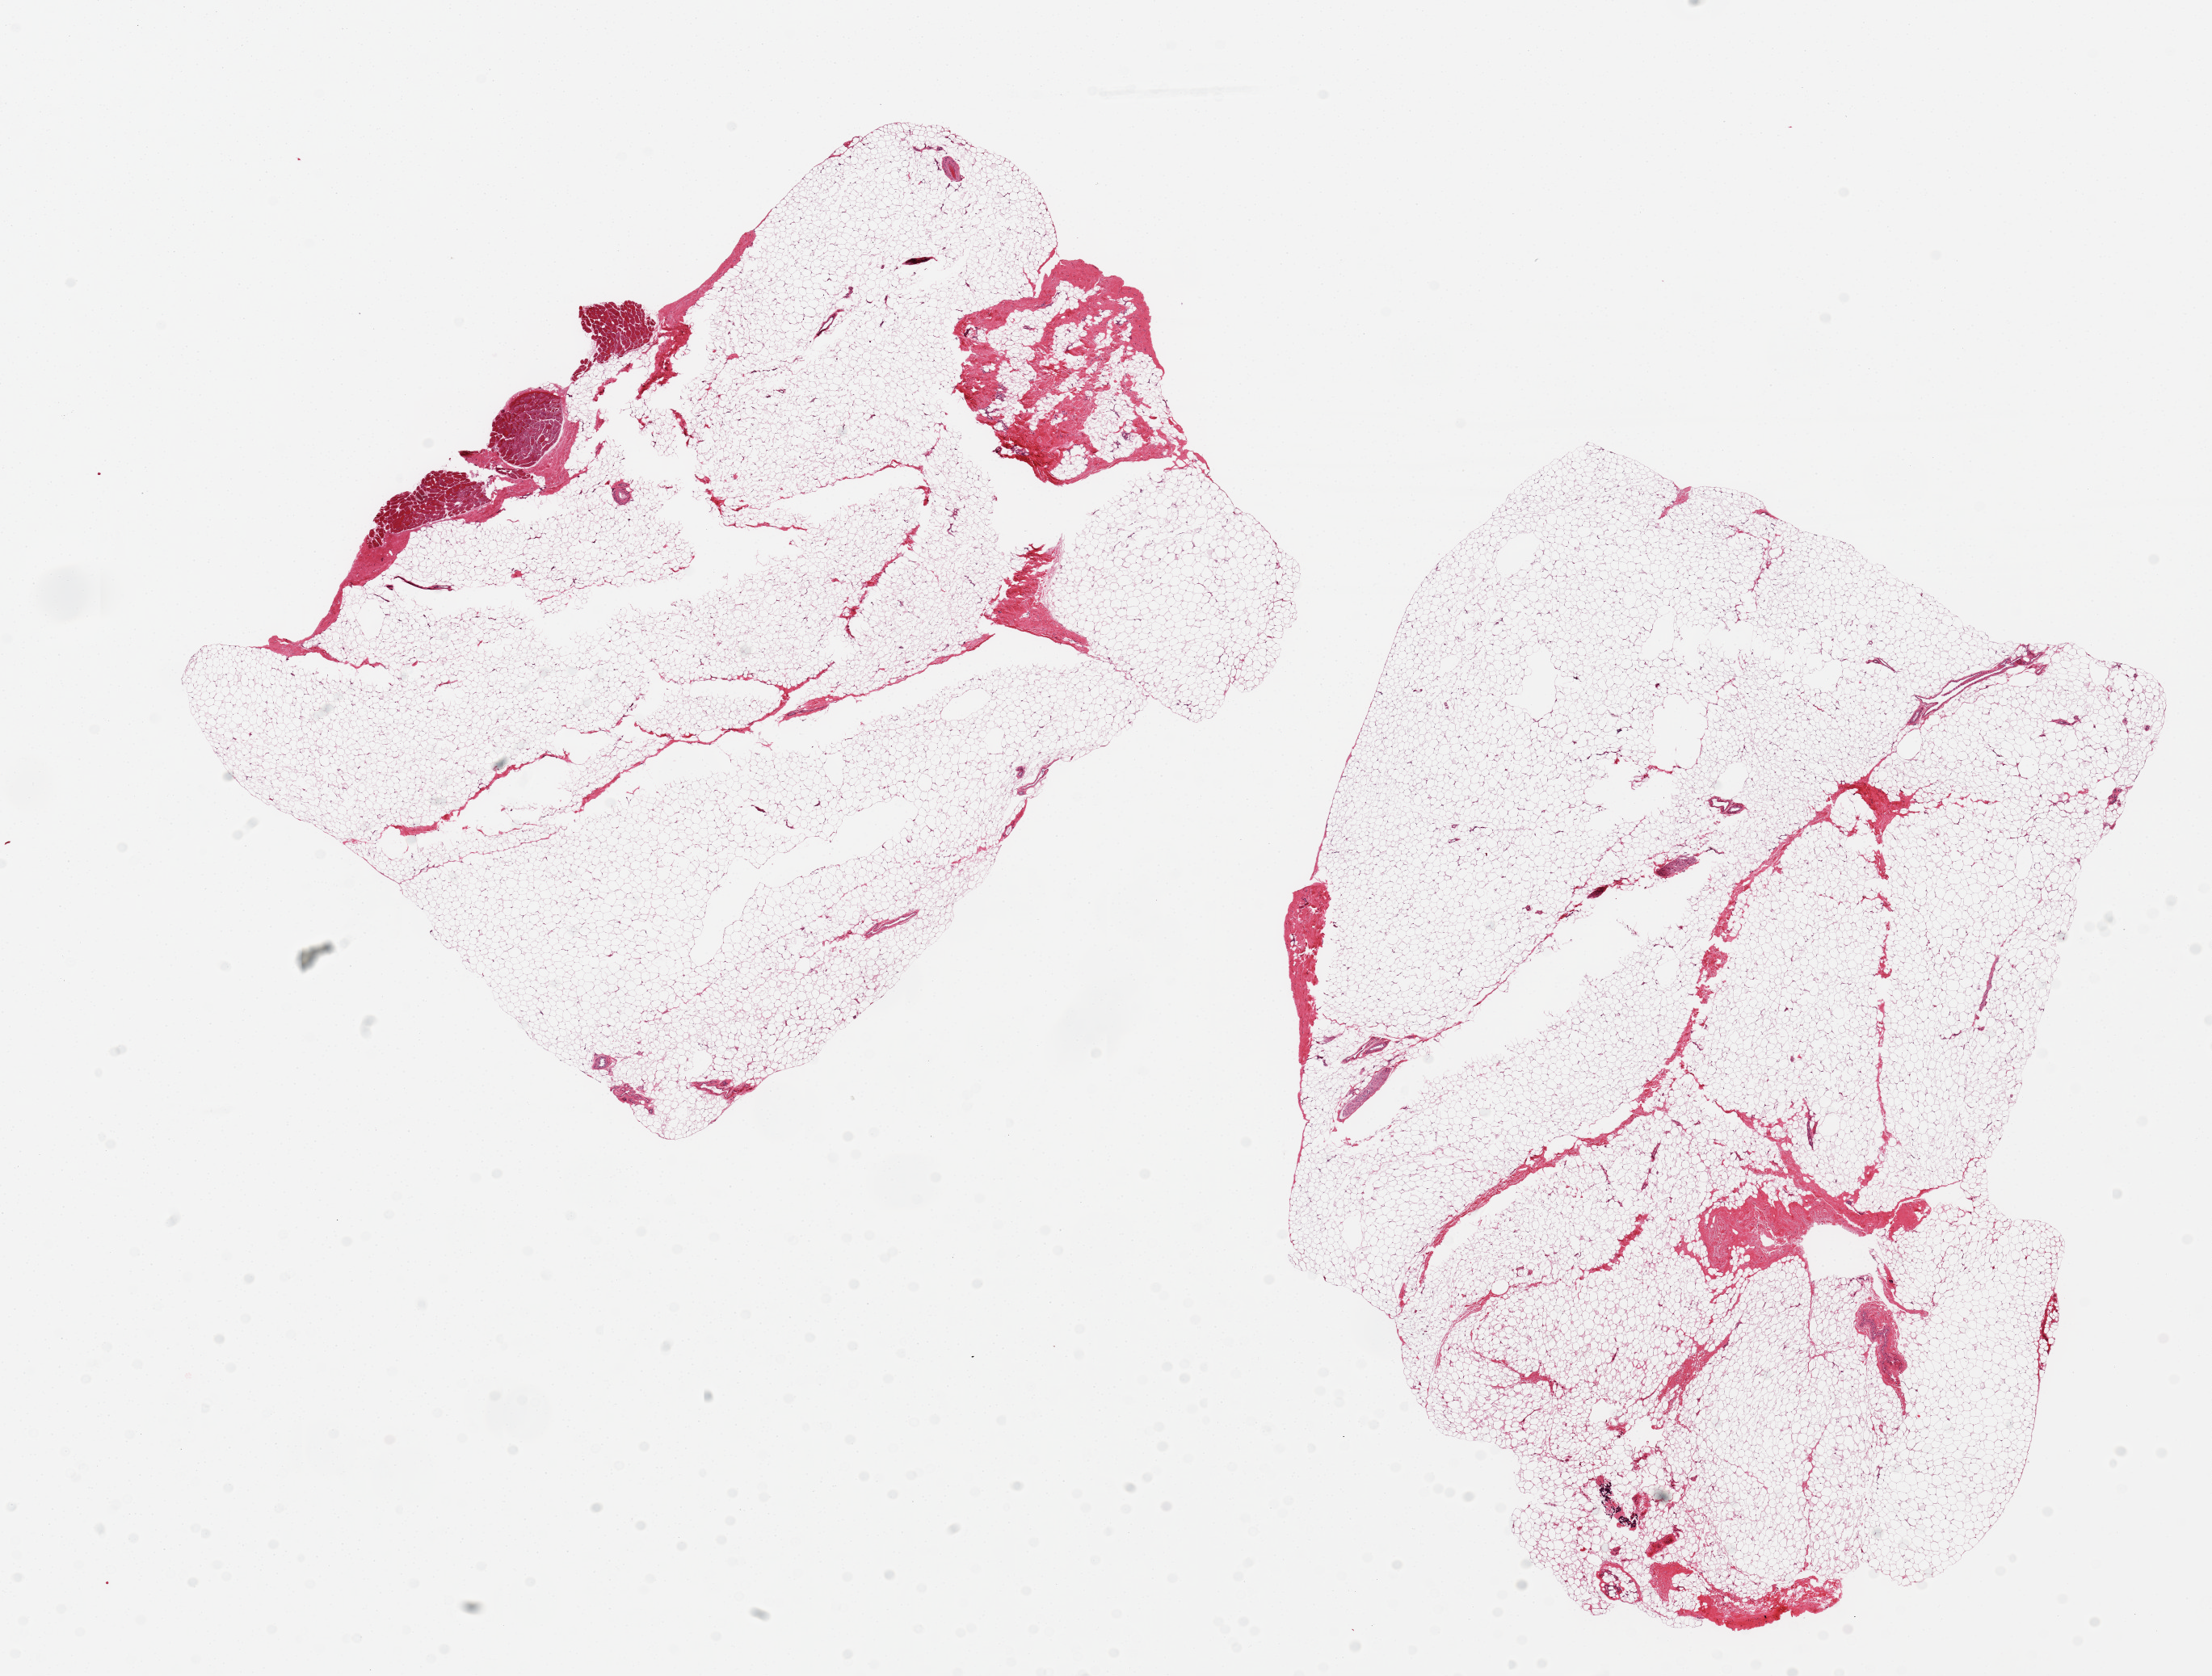
Whole-slide image, hematoxylin and eosin (H&E) stain — low-resolution overview of the scanned area, about 21.7 x 16.4 mm; PAXgene-fixed, paraffin-embedded tissue; sampled site (target tissue): breast; tissue donor sample. Donor sex: male.
- review note (as recorded): 2 ~9x7mm aliquots. No mammary ductal/lobular elements; all adipose, trace skeletal muscle